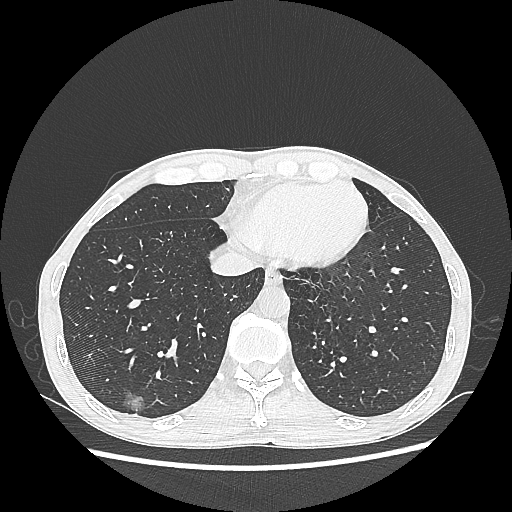
Chest CT, one axial slice; slice 75 of 270 in the series (ordered by position); reconstruction kernel LUNG; lung window (W 1500 / L -600 HU); 1.25 mm slice thickness; 512 × 512 image matrix, field of view 360 × 360 mm. Patient: male, 60 years. From the clinical record (not read from this slice): clinical TNM (as recorded): T1c N0 M0; histopathological grade: G2.
Outlined on this slice (rectangle marked by the reading radiologist):
- lung tumour (recorded histology: adenocarcinoma): box from (x=116, y=386) to (x=151, y=425) px